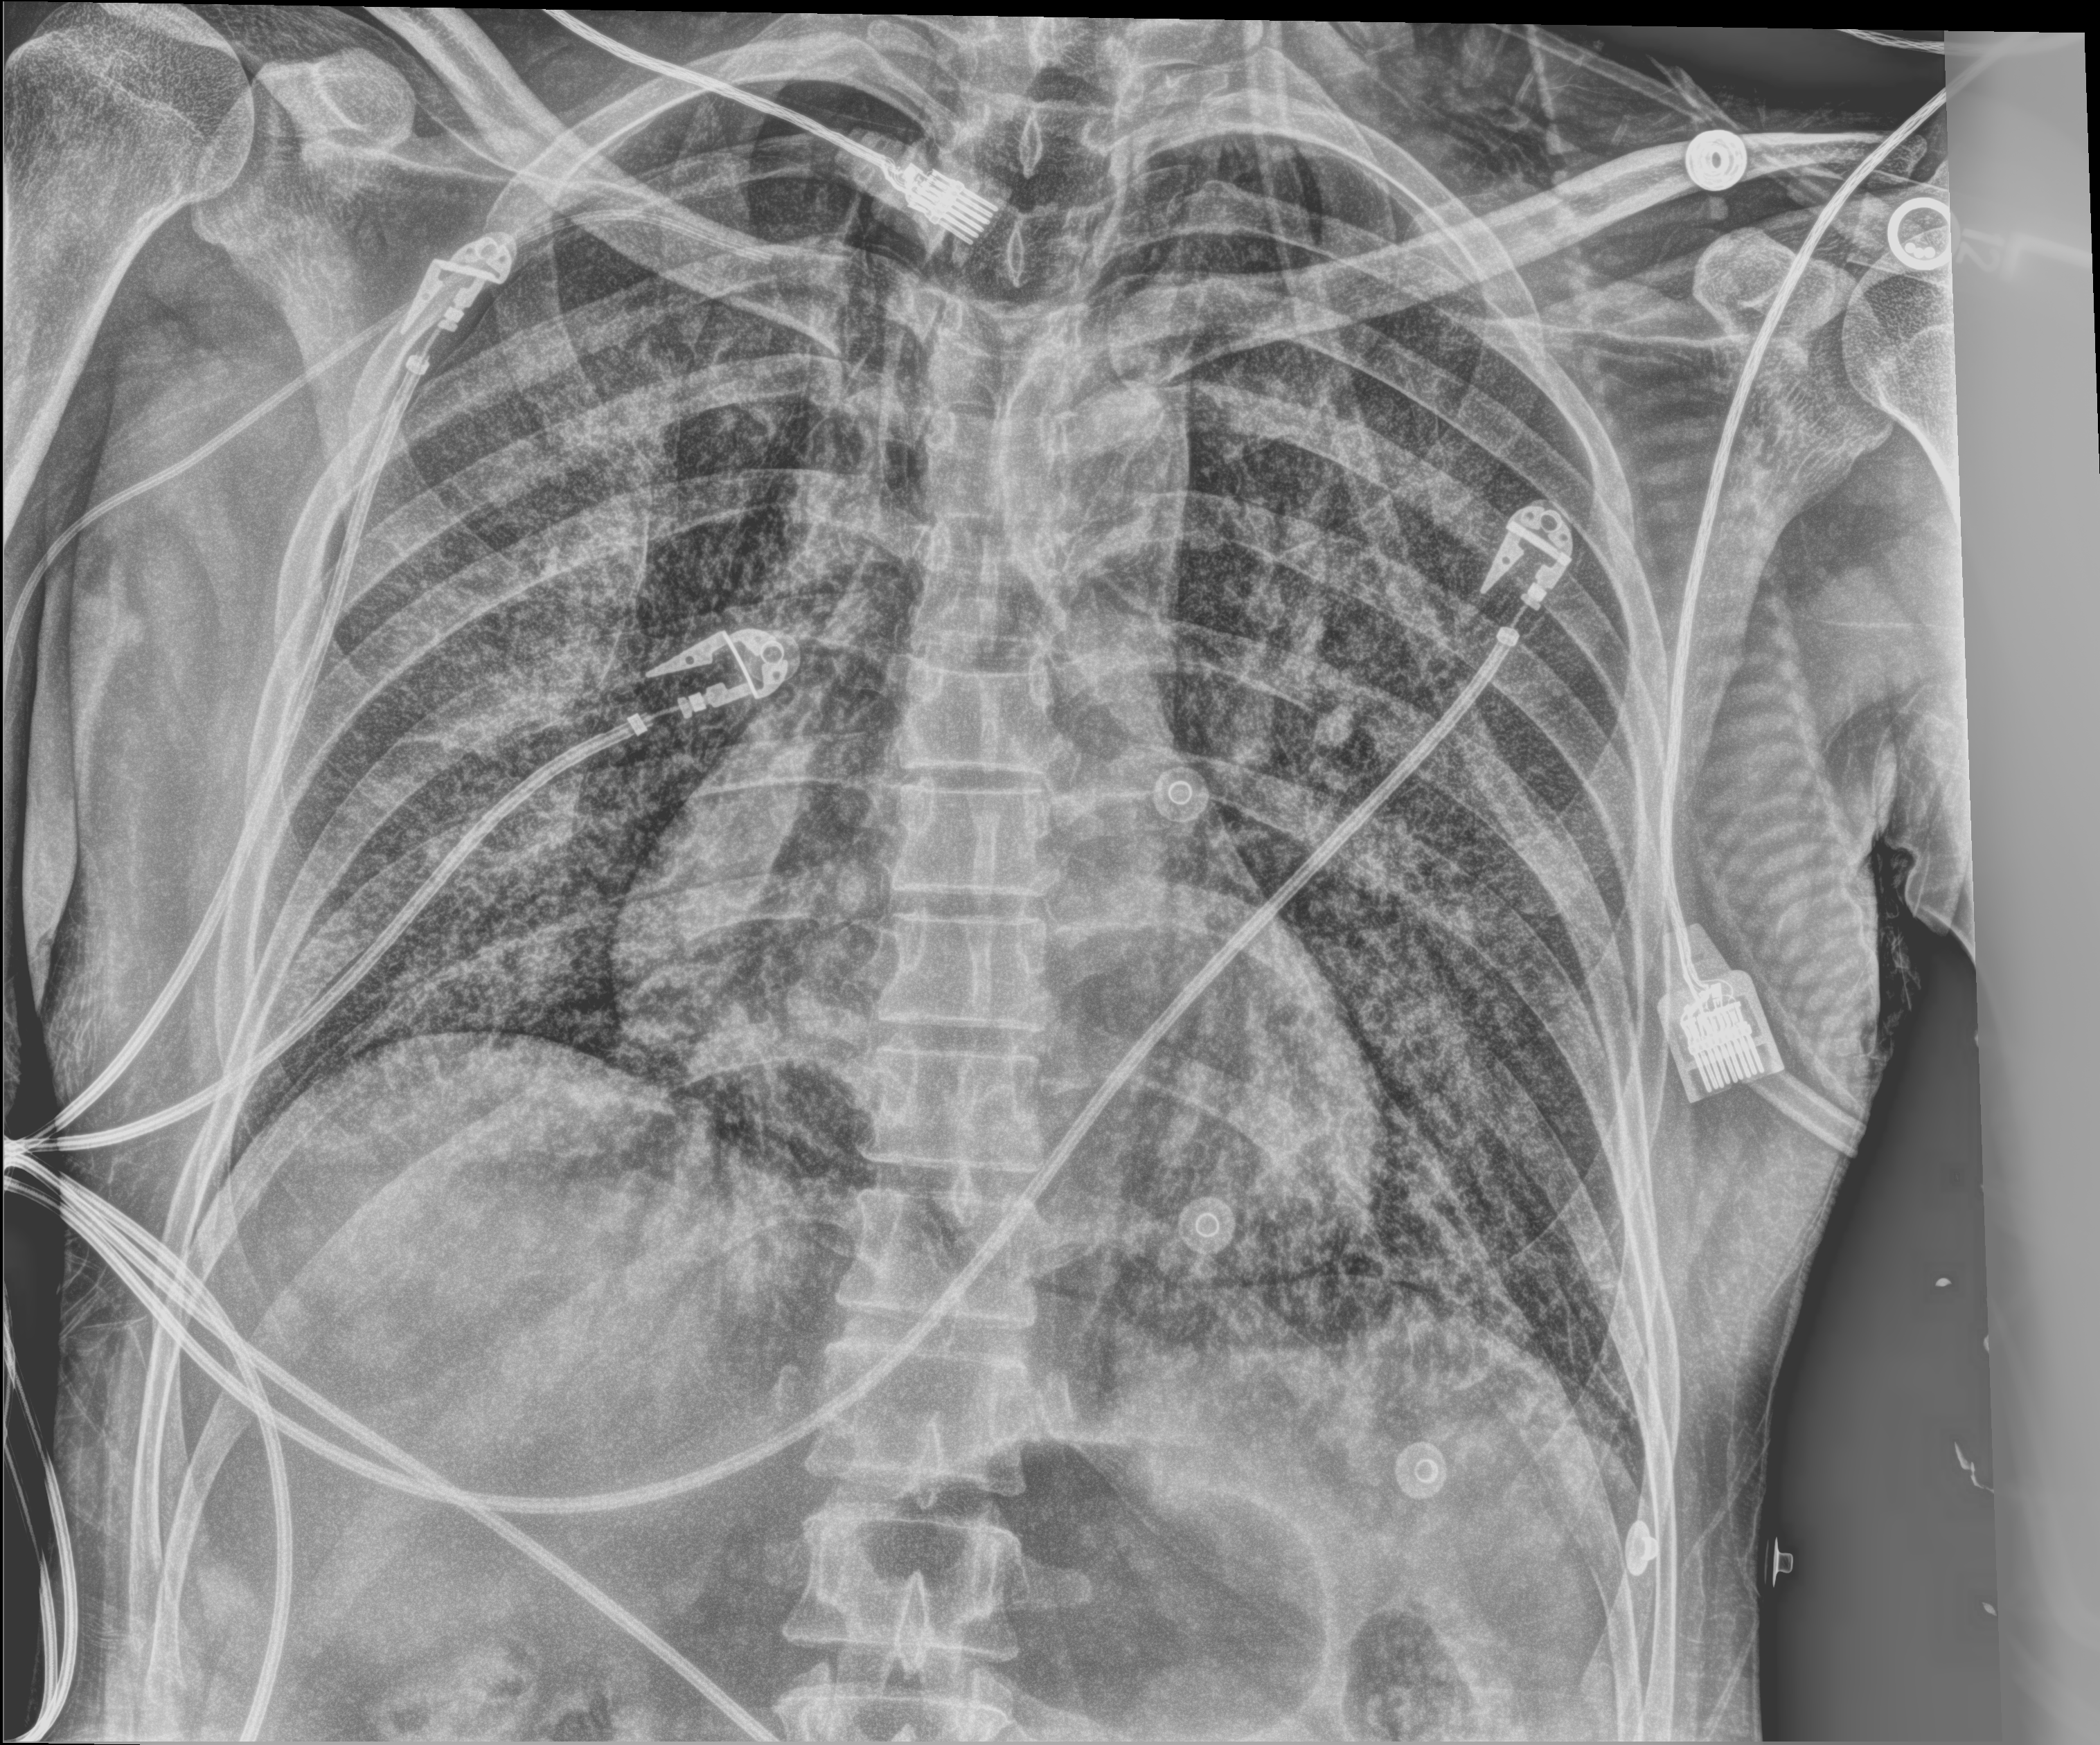
Chest X-ray (portable). Adult patient hospitalised with COVID-19, age 18–59 years.
Hospital-stay facts (about this admission, not read from this image; timing relative to this image not recorded): admitted to intensive care during this hospital stay: yes.